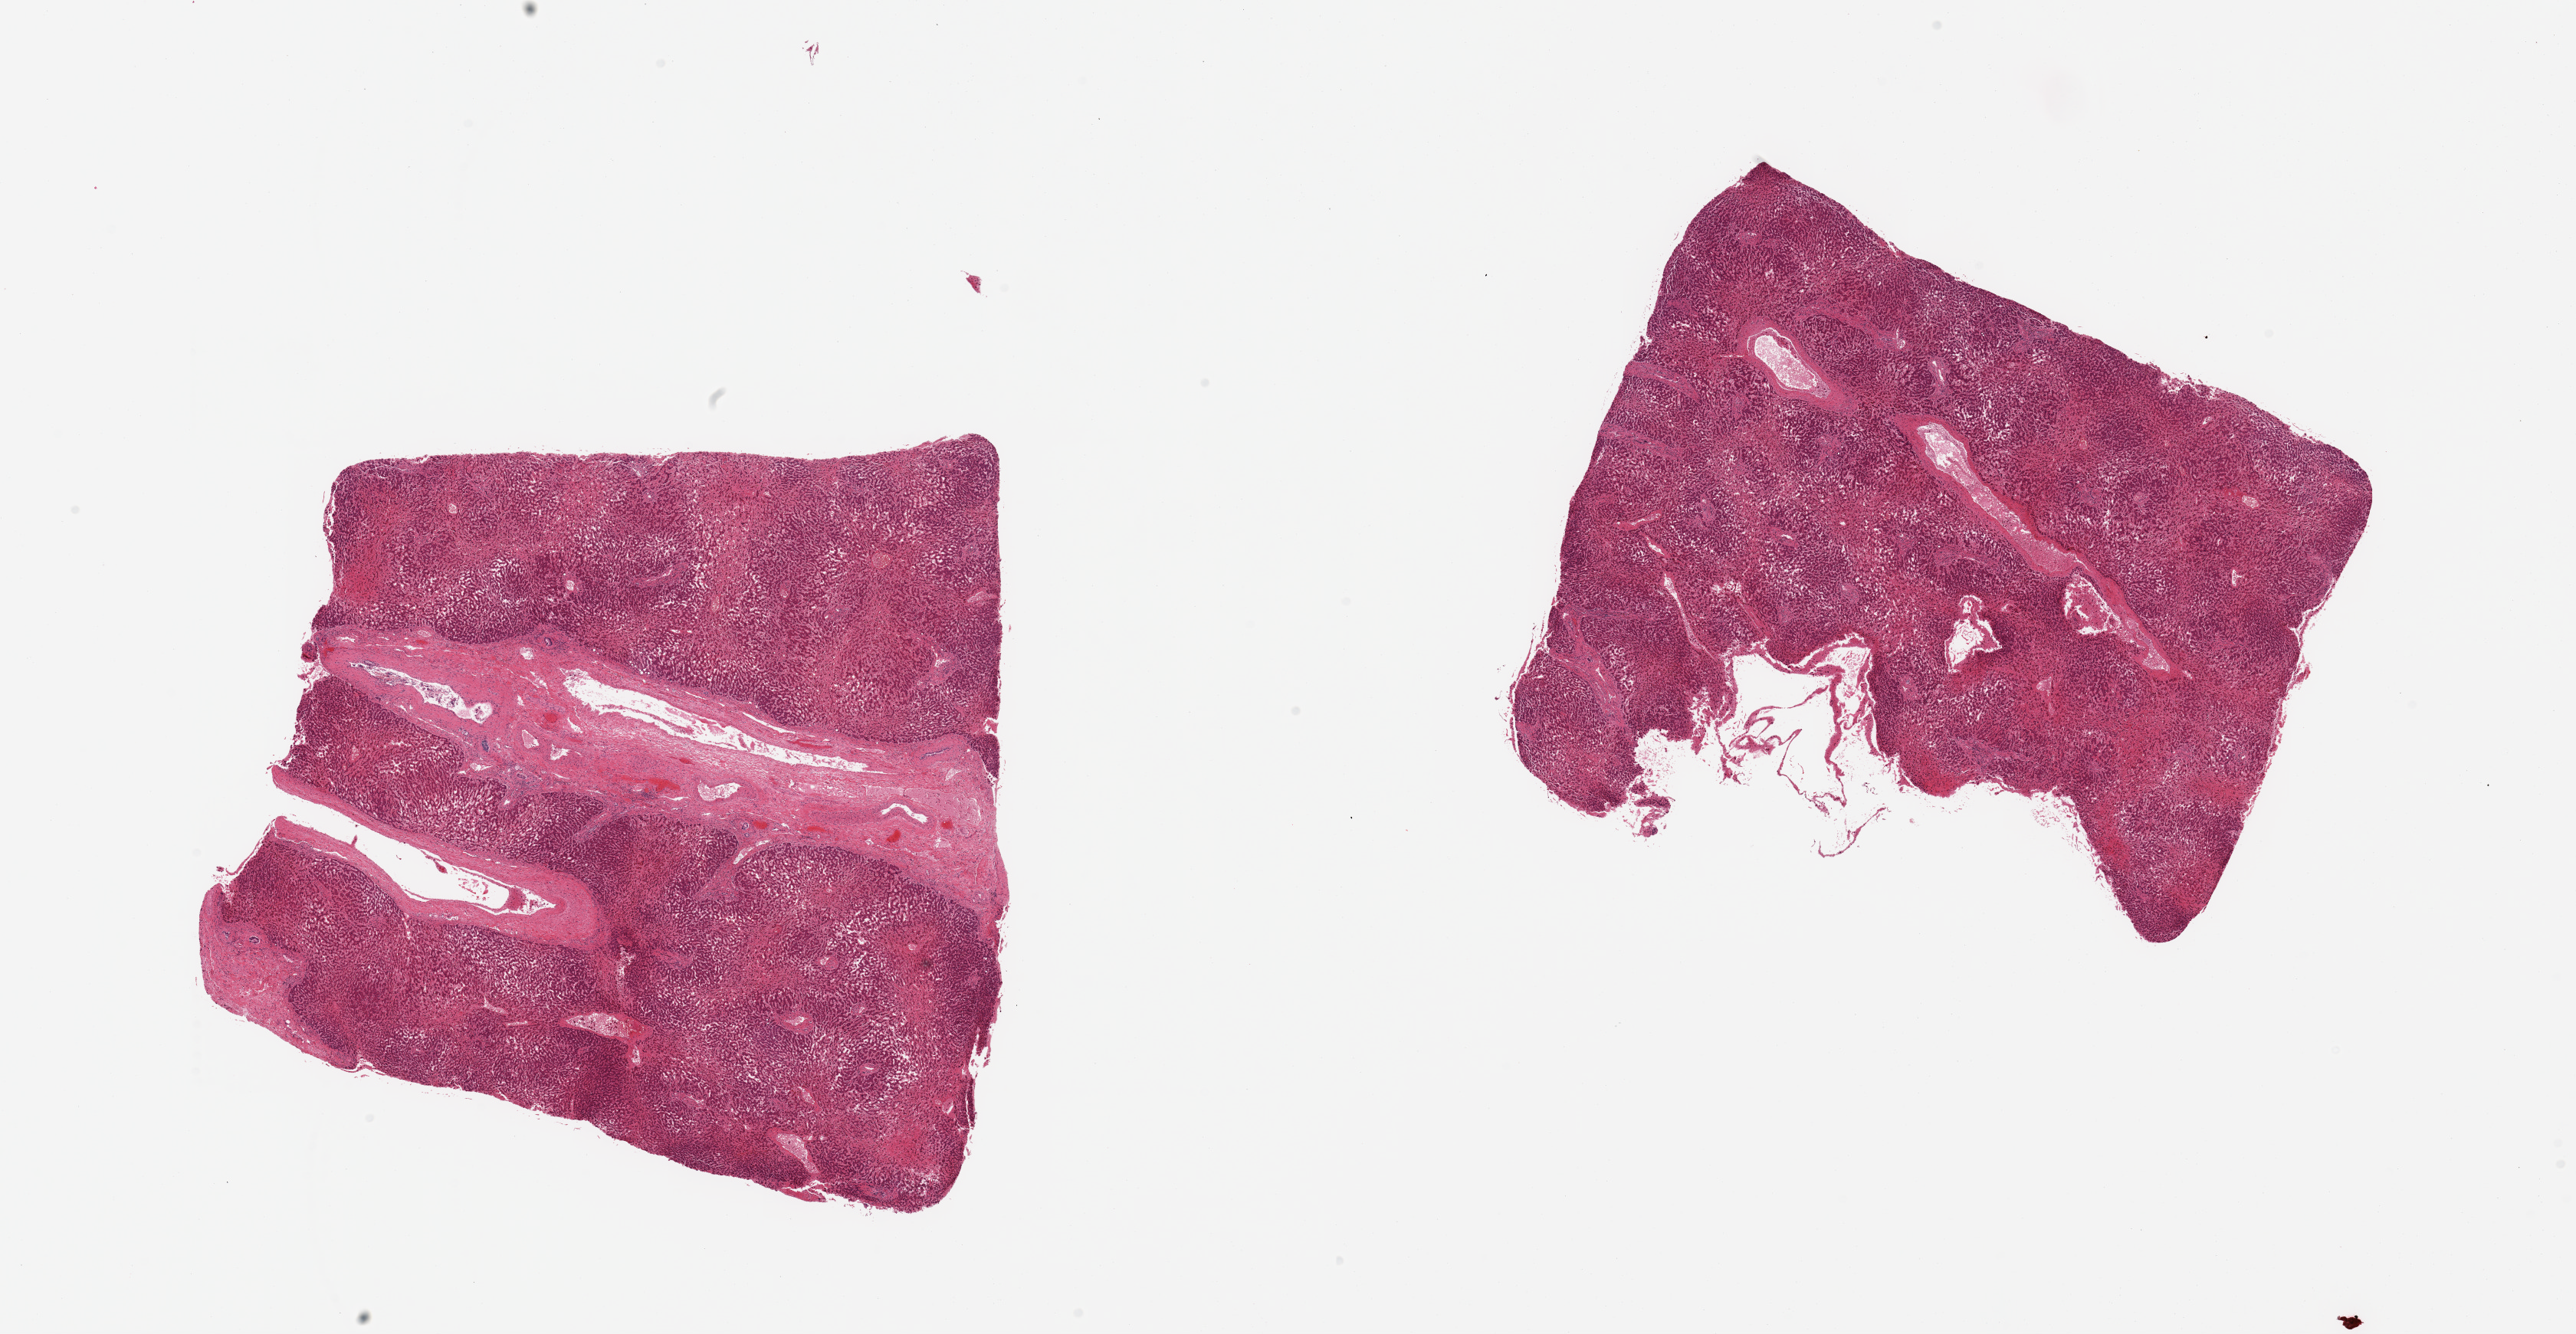
Hematoxylin and eosin (H&E) whole-slide image, a low-resolution overview of the entire scanned area, about 26.6 x 13.8 mm (acquisition: 20x scan); PAXgene-fixed, paraffin-embedded tissue; section of liver (target tissue); donor tissue sample. Donor sex: male.
Pathologist's review note for this sample: 2 pieces; severe central congestion & atrophy.